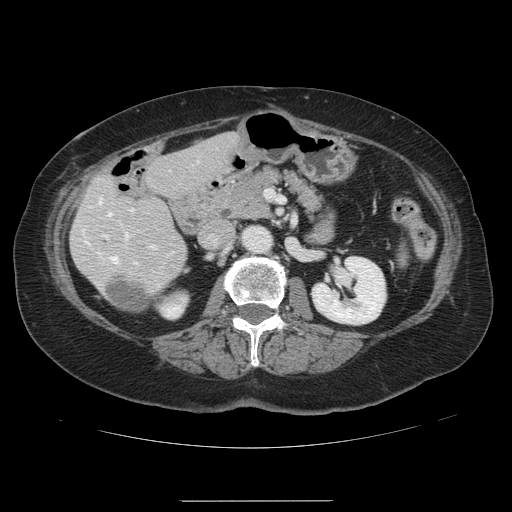
Contrast-enhanced abdominal CT, one axial slice. Position 51 of 141 along the scan axis. 120 kVp. Intravenous contrast given. Soft-tissue window (W 400 / L 40 HU). 512 × 512 image matrix. Female patient, age 74 years. Case-level facts recorded for this patient, not image findings: diagnosis: colorectal cancer liver metastases, imaged before liver resection.
Structures marked on this image (expert manual segmentation):
- hepatic veins: bounding box (x1, y1, x2, y2) in pixels: (99, 199, 128, 262)
- liver: (71, 134, 239, 313)
- planned liver remnant (the part of the liver to remain after resection): (71, 134, 239, 313)
- portal vein (with intrahepatic branches): (104, 209, 155, 248)
- liver metastasis: (109, 278, 158, 309)